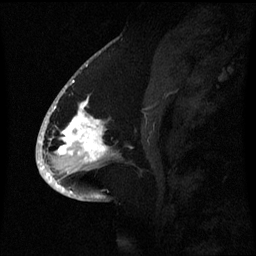
Breast MRI (dynamic contrast-enhanced), one sagittal slice; slice 33 of 60 in the series (ordered by position); dynamic contrast-enhanced series, image 2 of 3 at this slice position (ordered by acquisition); 1.5 T; TE 4.2 ms, TR 8.4 ms; 2.1 mm slice thickness; 256 × 256 image matrix. Patient: female, 53 years. Case-level facts recorded for this patient, not image findings: setting: breast cancer imaged before/during neoadjuvant chemotherapy; receptor status: HR-positive, HER2-negative.
Structures marked on this image (semi-automatic segmentation, software-assisted and operator-edited):
- analysis volume of interest (the breast-tissue region the enhancement analysis was run in; not a lesion): box from (x=52, y=90) to (x=119, y=171) px
- tumour enhancement mask (voxels above the 70 % enhancement threshold inside the analysis volume of interest): (x=54, y=90)–(x=109, y=161)